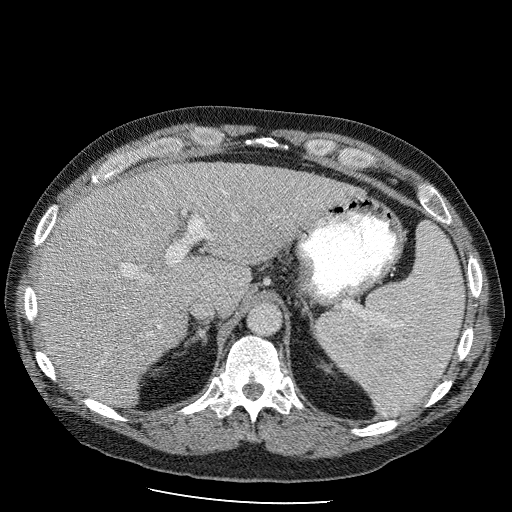
Contrast-enhanced abdominal CT (liver protocol), one axial slice. Position 70 of 98 along the scan axis. Reconstruction kernel STANDARD. Soft-tissue window (W 400 / L 40 HU). 2.5 mm slice thickness. 512 × 512 image matrix. From the clinical record (not read from this slice): diagnosis: hepatocellular carcinoma (patient treated with transarterial chemoembolisation; whether this scan precedes or follows treatment is not stated here); TNM stage (as recorded): Stage-II; Child-Pugh class: B; tumour differentiation: moderately differentiated; tumour nodularity: uninodular.
Outlined on this slice (semi-automatic segmentation, software-assisted and operator-edited):
- liver parenchyma outside the tumour (the mass and vessels are separate outlines, so this box may not span the whole liver): bounding box <36,162,362,408> (left, top, right, bottom; pixels)
- mass: <84,307,142,358>
- liver vessels: <124,226,211,329>